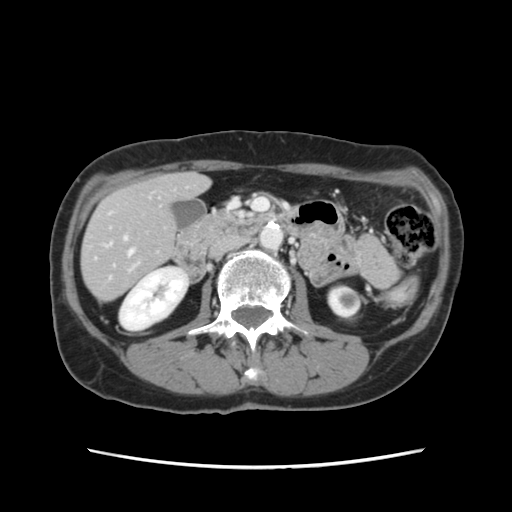
Contrast-enhanced abdominal CT, one axial slice. Position 41 of 120 along the scan axis. Intravenous contrast given. Soft-tissue window (W 400 / L 40 HU). 2.5 mm slice thickness. 512 × 512 image matrix, field of view 330 × 330 mm. Female patient, age 70 years. From the clinical record (not read from this slice): diagnosis: colorectal cancer liver metastases, imaged before liver resection; multiple liver metastases: no; largest metastasis: 2.5 cm; disease in both lobes: no.
Annotated regions visible in this slice (expert manual segmentation):
- hepatic veins: box from (x=107, y=243) to (x=134, y=256) px
- liver: (x=82, y=174)–(x=208, y=300)
- planned liver remnant (the part of the liver to remain after resection): (x=82, y=174)–(x=207, y=300)
- portal vein (with intrahepatic branches): (x=124, y=237)–(x=127, y=240)